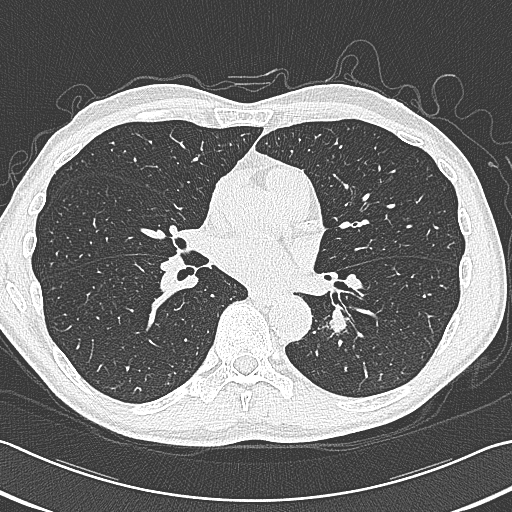
Axial slice from a low-dose chest CT screening exam; baseline annual screen; lung window (W 1500 / L -600 HU); lung (sharp) reconstruction kernel (B80f); 120 kVp; slice 183 of 354 in the series; 512 × 512 image matrix, field of view 346 × 346 mm. Male participant, aged 59 years at enrolment. Former smoker at enrolment.
Expert-annotated lung lesion, box from (x=312, y=296) to (x=376, y=353) px. Screening reader's record for this exam (one nodule recorded; not confirmed to be the boxed lesion): non-calcified nodule or mass ≥4 mm, left lower lobe, 15 × 15 mm, smooth margins, soft tissue attenuation.